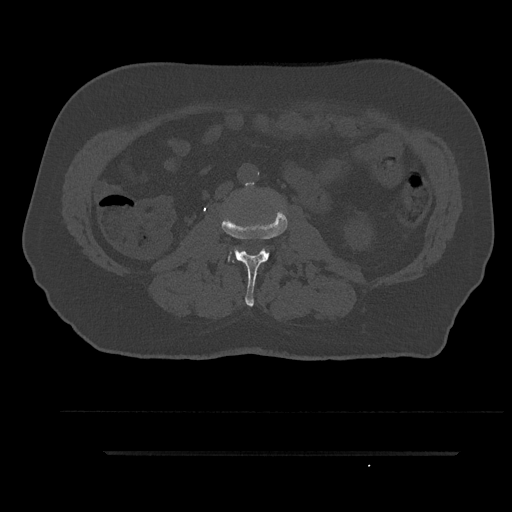
CT including the spine, one axial slice; slice 89 of 797 in the series (ordered by position); reconstruction kernel Br40s/3; bone window (W 1800 / L 400 HU); 0.5 mm slice thickness; 512 × 512 image matrix. Patient: male, 63 years. Case-level facts recorded for this patient, not image findings: primary cancer: renal.
Outlined on this slice (semi-automatically segmented with operator editing):
- L2 vertebra: bounding box <221,209,288,307> (left, top, right, bottom; pixels)
- L3 vertebra: <228,253,231,261>